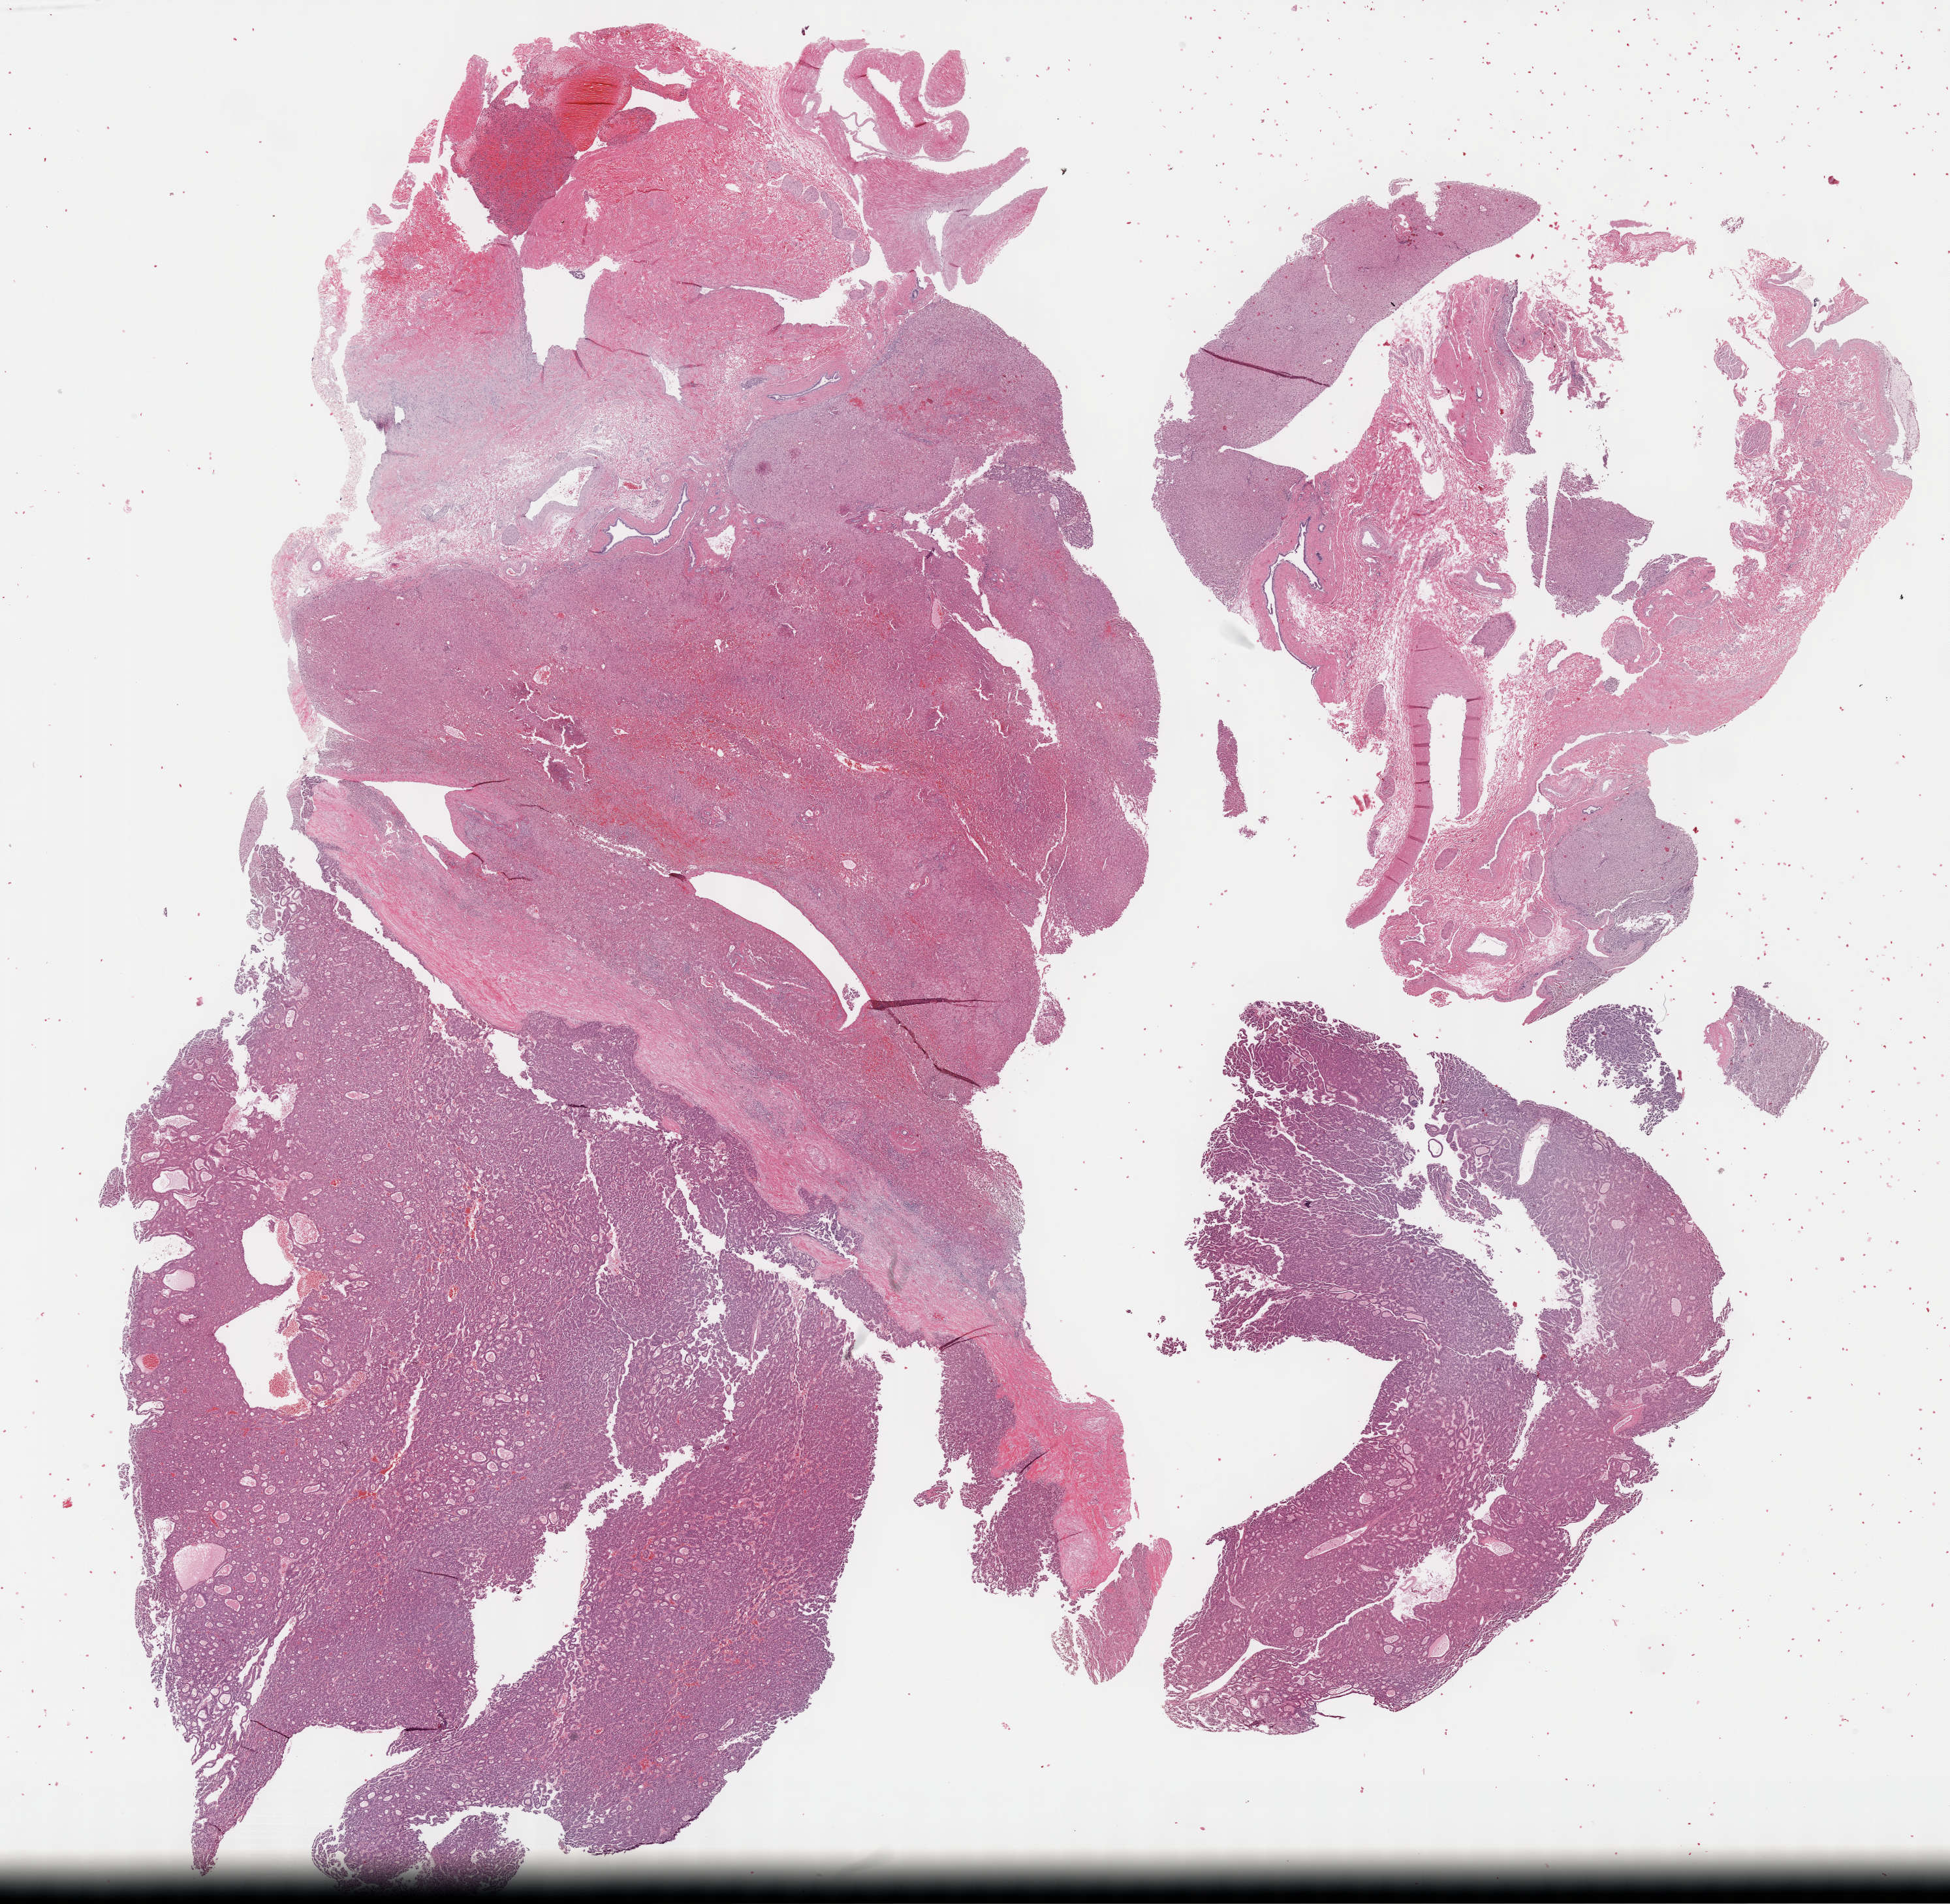
Hematoxylin and eosin (H&E) stained whole-slide image — a low-resolution overview of the entire scanned area, about 24.2 x 23.6 mm (from a 40x scan), formalin-fixed paraffin-embedded (FFPE) diagnostic section, sample: primary tumour, liver. Patient: female, age at initial diagnosis 61 years. Histologic grade: G2 (moderately differentiated).
- TNM: T1 N0 M0
- histologic diagnosis: Hepatocellular carcinoma, NOS
- AJCC pathologic stage: I (6th edition)